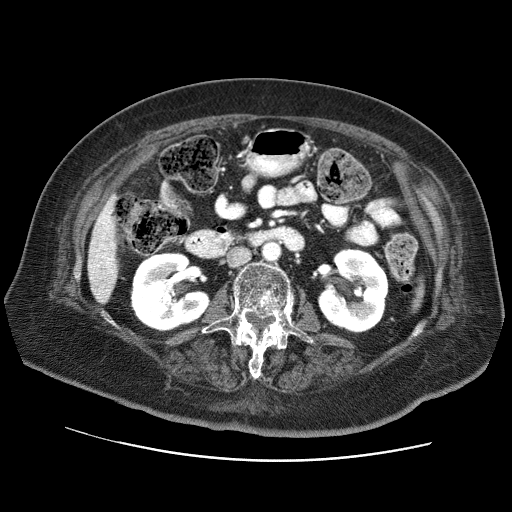
Contrast-enhanced abdominal CT (liver protocol), one axial slice; position 19 of 73 along the scan axis; soft-tissue window (W 400 / L 40 HU); 2.5 mm slice thickness; 512 × 512 image matrix, field of view 380 × 380 mm. Case-level facts recorded for this patient, not image findings: diagnosis: hepatocellular carcinoma (patient treated with transarterial chemoembolisation; whether this scan precedes or follows treatment is not stated here); TNM stage (as recorded): Stage-I; Child-Pugh class: A; tumour differentiation: well differentiated; tumour nodularity: uninodular.
Outlined on this slice (semi-automatically segmented with operator editing):
- liver parenchyma outside the tumour (the mass and vessels are separate outlines, so this box may not span the whole liver): bounding box [x1, y1, x2, y2] px = [88, 195, 118, 304]
- liver vessels: [101, 212, 113, 272]